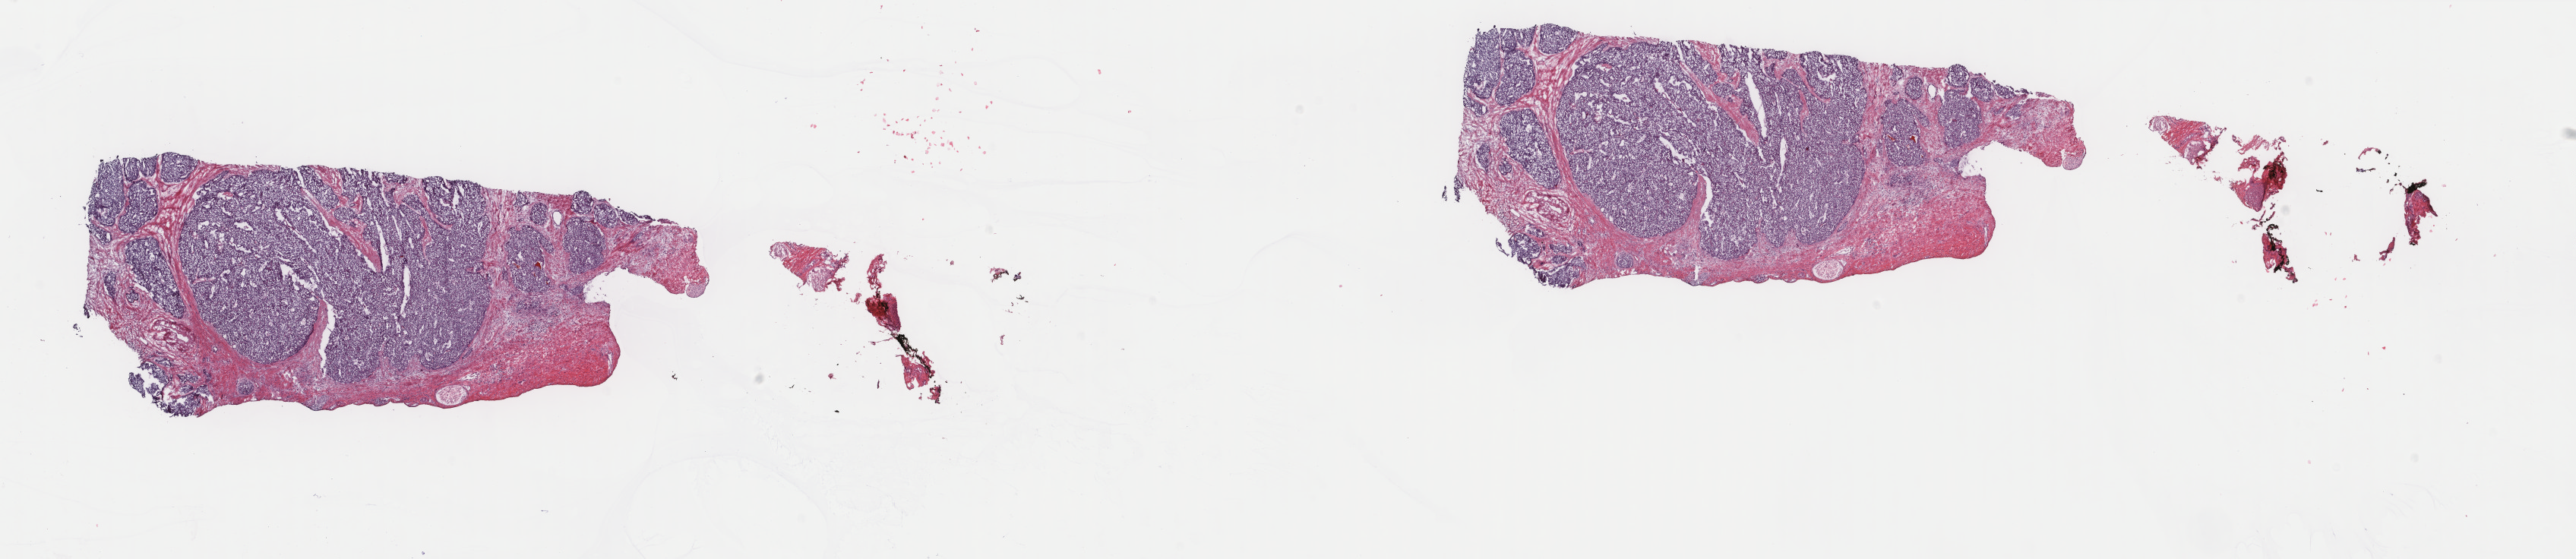
Hematoxylin and eosin (H&E) stained whole-slide image, shown as a low-resolution overview of the whole scanned area (about 26.9 x 5.8 mm, acquisition: 40x scan). Frozen section from the top of the tissue portion. Sample: primary tumour, prostate. Male patient; age at initial diagnosis 66 years. Gleason score: 8 (4+4). Composition of this section per pathologist review: tumour cells 85%, tumour nuclei 95%, normal cells 0%, stromal cells 15%, necrosis 0%. Inflammatory infiltration, as recorded: lymphocyte infiltration 2%, monocyte infiltration 3%, neutrophil infiltration 0%.
- pathologic diagnosis: Infiltrating duct carcinoma, NOS (prostate gland)